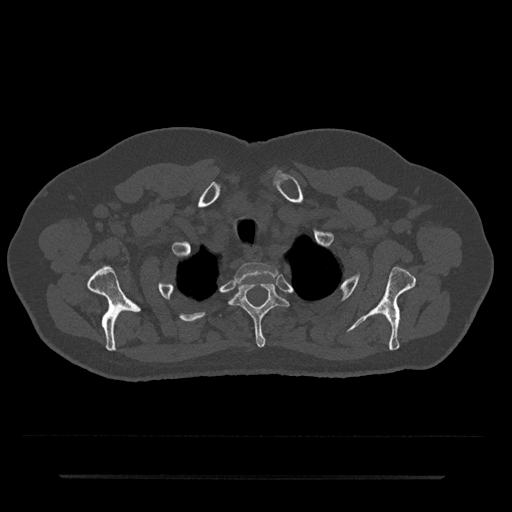
CT including the spine, one axial slice. Position 609 of 797 along the scan axis. Reconstruction kernel Br40s/3. 120 kVp. Bone window (W 1800 / L 400 HU). 0.5 mm slice thickness. 512 × 512 image matrix, field of view 437 × 437 mm. Male patient, age 69 years. Case-level facts recorded for this patient, not image findings: primary cancer: prostate.
Outlined on this slice (semi-automatically segmented with operator editing):
- T1 vertebra: bounding box [x1, y1, x2, y2] px = [235, 262, 279, 284]
- T2 vertebra: [229, 283, 289, 347]